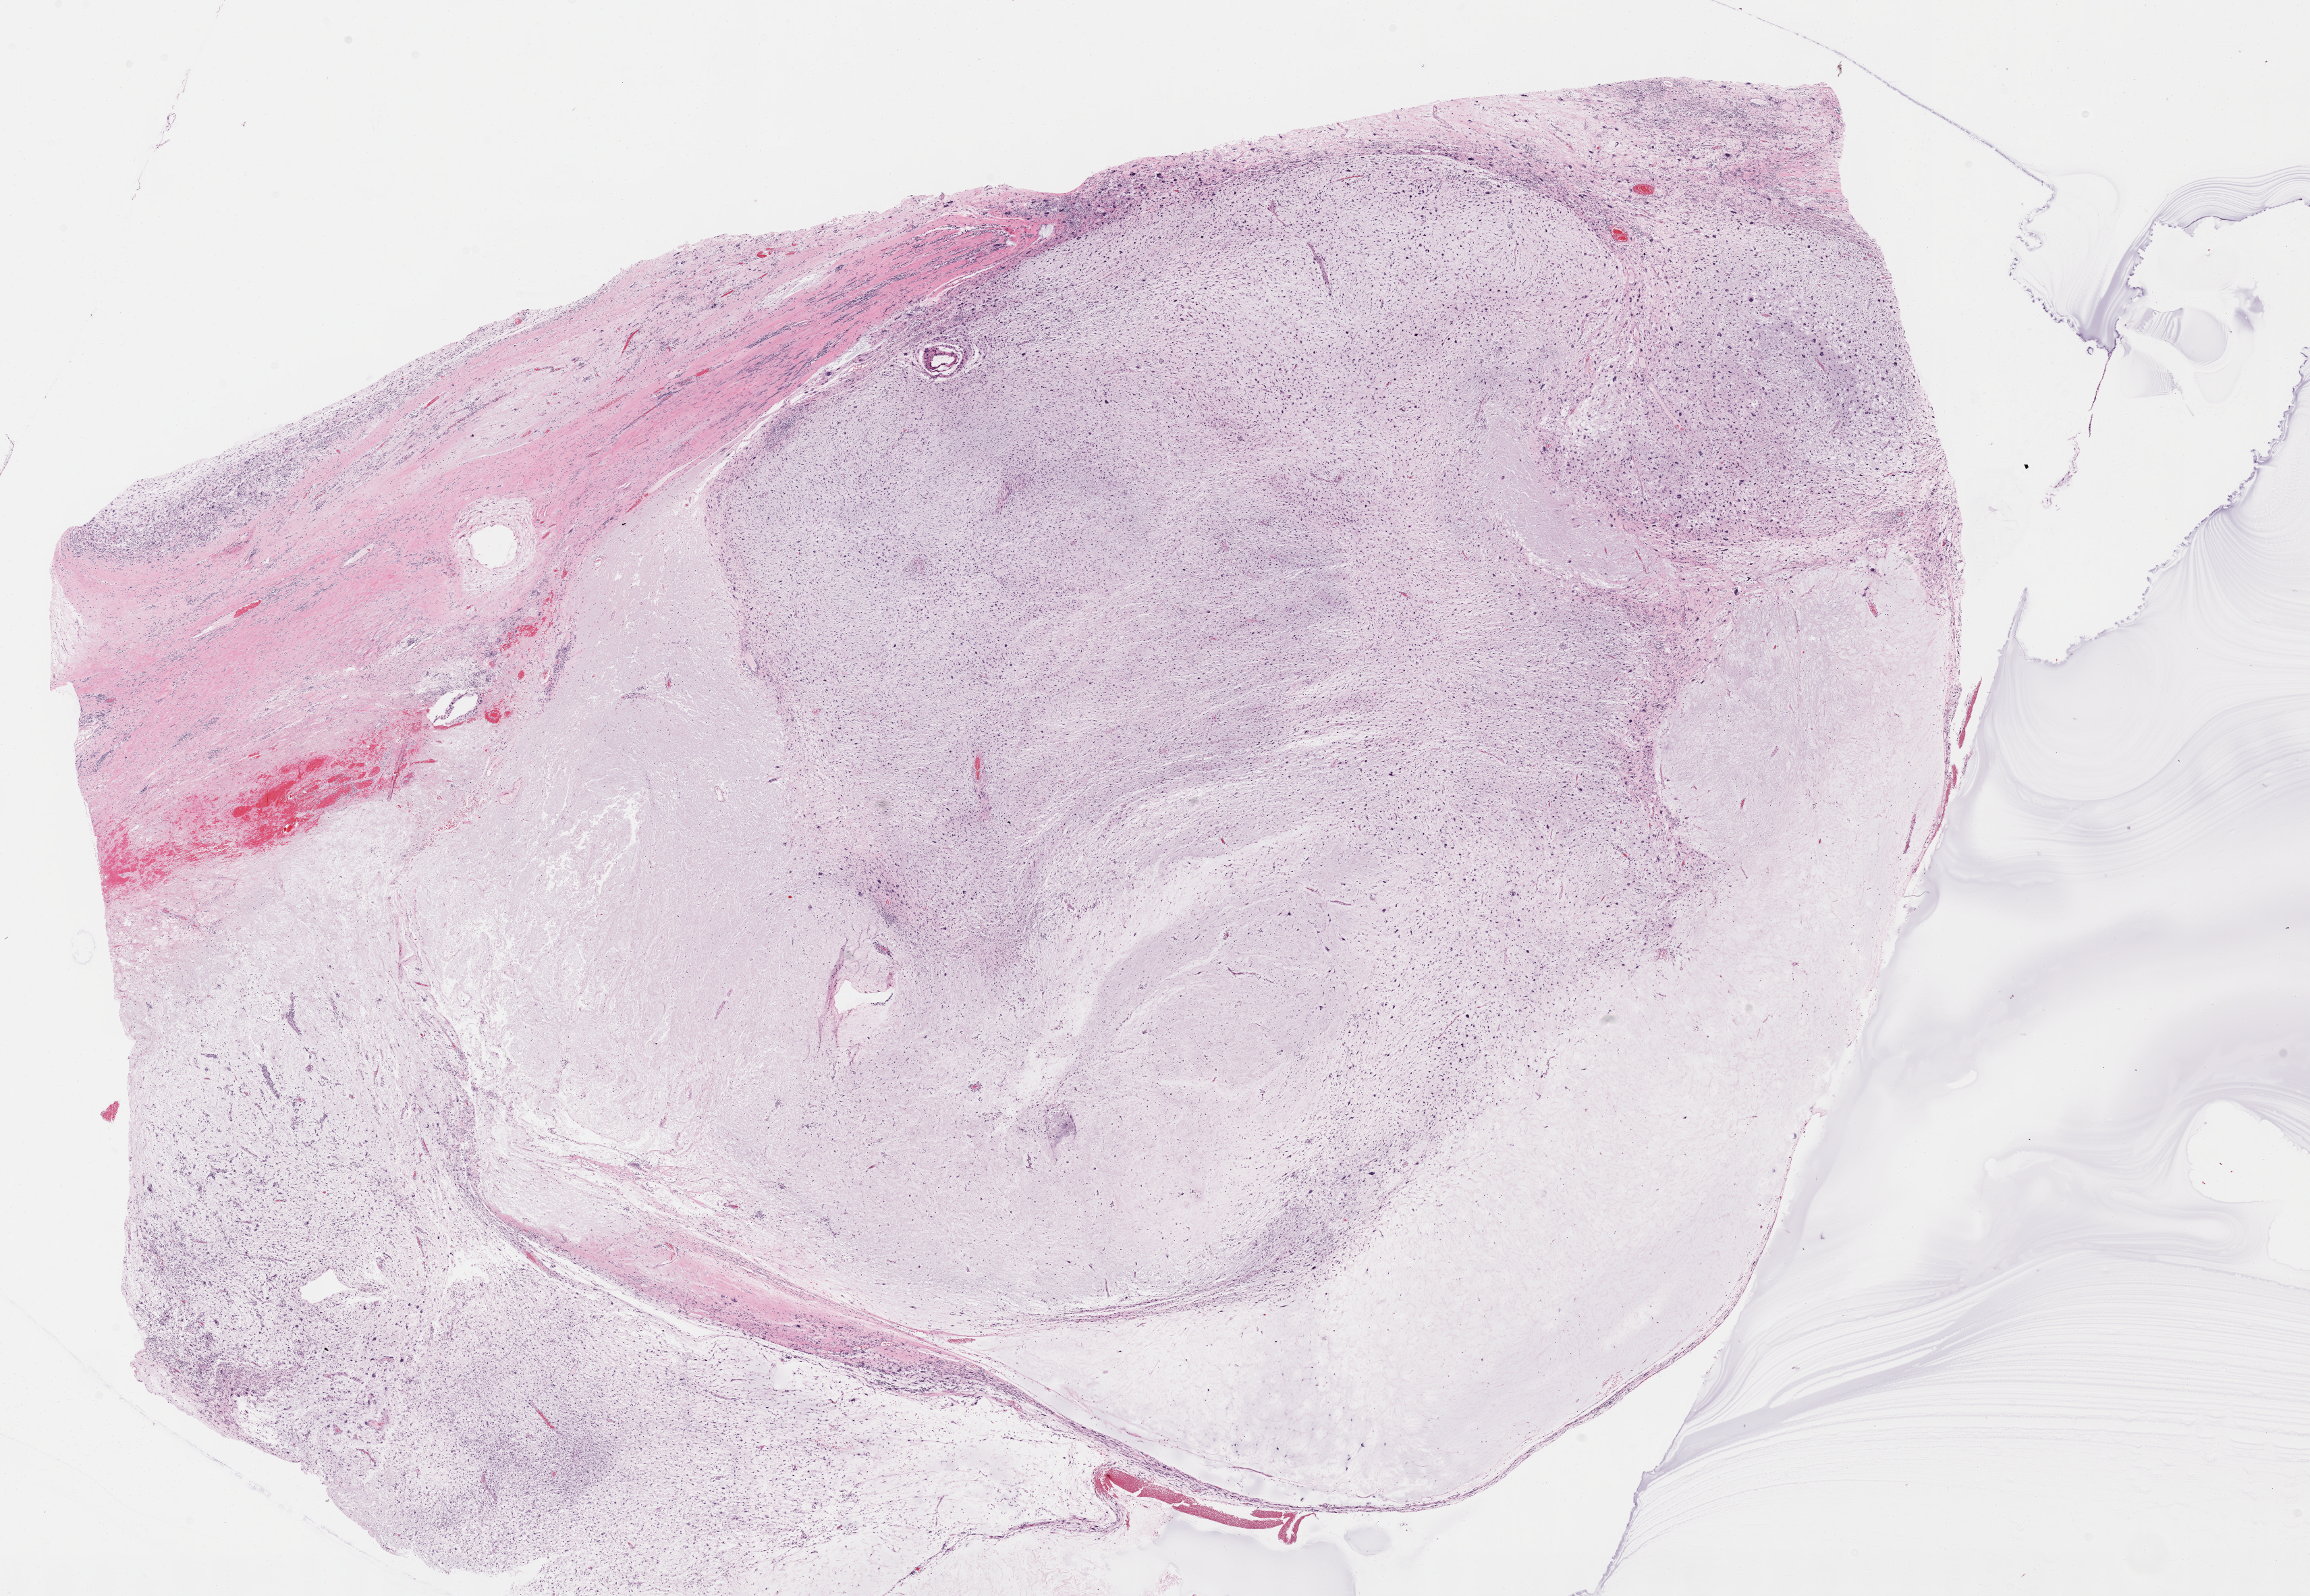
Whole-slide histology image, Hematoxylin and eosin (H&E) stained — a low-resolution overview of the entire scanned area, about 27.7 x 19.1 mm (acquisition: 40x scan). Formalin-fixed paraffin-embedded (FFPE) diagnostic section. Connective, subcutaneous and other soft tissues, primary tumour sample. Female, age 83 years at initial diagnosis.
• diagnosis: Fibromyxosarcoma (connective, subcutaneous and other soft tissues of lower limb and hip)